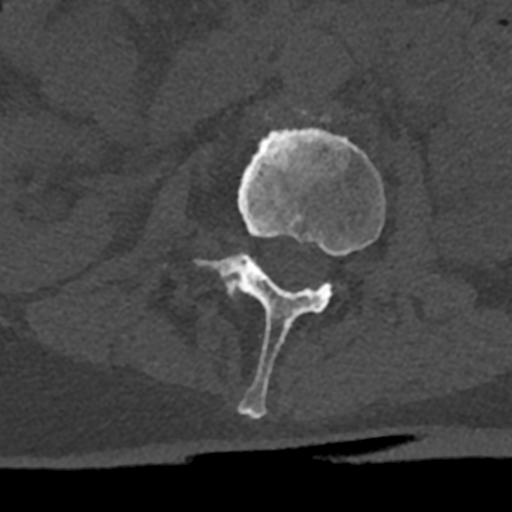
CT including the spine, one axial slice. Position 369 of 797 along the scan axis. Reconstruction kernel Br40s/3. 120 kVp. Bone window (W 1800 / L 400 HU). 0.5 mm slice thickness. 512 × 512 image matrix. Male patient, age 74 years. Case-level facts recorded for this patient, not image findings: primary cancer: renal; vertebrae with lytic lesions (as recorded): T10, L1, L2, L3, L4, L5.
Outlined on this slice (semi-automatic segmentation, software-assisted and operator-edited):
- L2 vertebra: bounding box (x1, y1, x2, y2) in pixels: (194, 109, 385, 419)
- L3 vertebra: (223, 251, 249, 295)